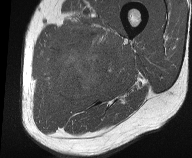
MRI of an extremity soft-tissue mass, one axial slice. Slice 17 of 61 in the series (ordered by position). MR volume resampled by the dataset authors to the PET/CT grid (not the native acquisition matrix). 192 × 158 image matrix, field of view 187 × 154 mm. Male patient. From the clinical record (not read from this slice): histological type: pleiomorphic liposarcoma; grade: high; site of the primary tumour: left thigh.
Outlined on this slice (expert contour drawn on MRI and transferred to this co-registered scan by the dataset authors):
- gross tumour volume including surrounding oedema: bounding box <45,19,124,104> (left, top, right, bottom; pixels)
- gross tumour volume (mass): <50,46,106,99>